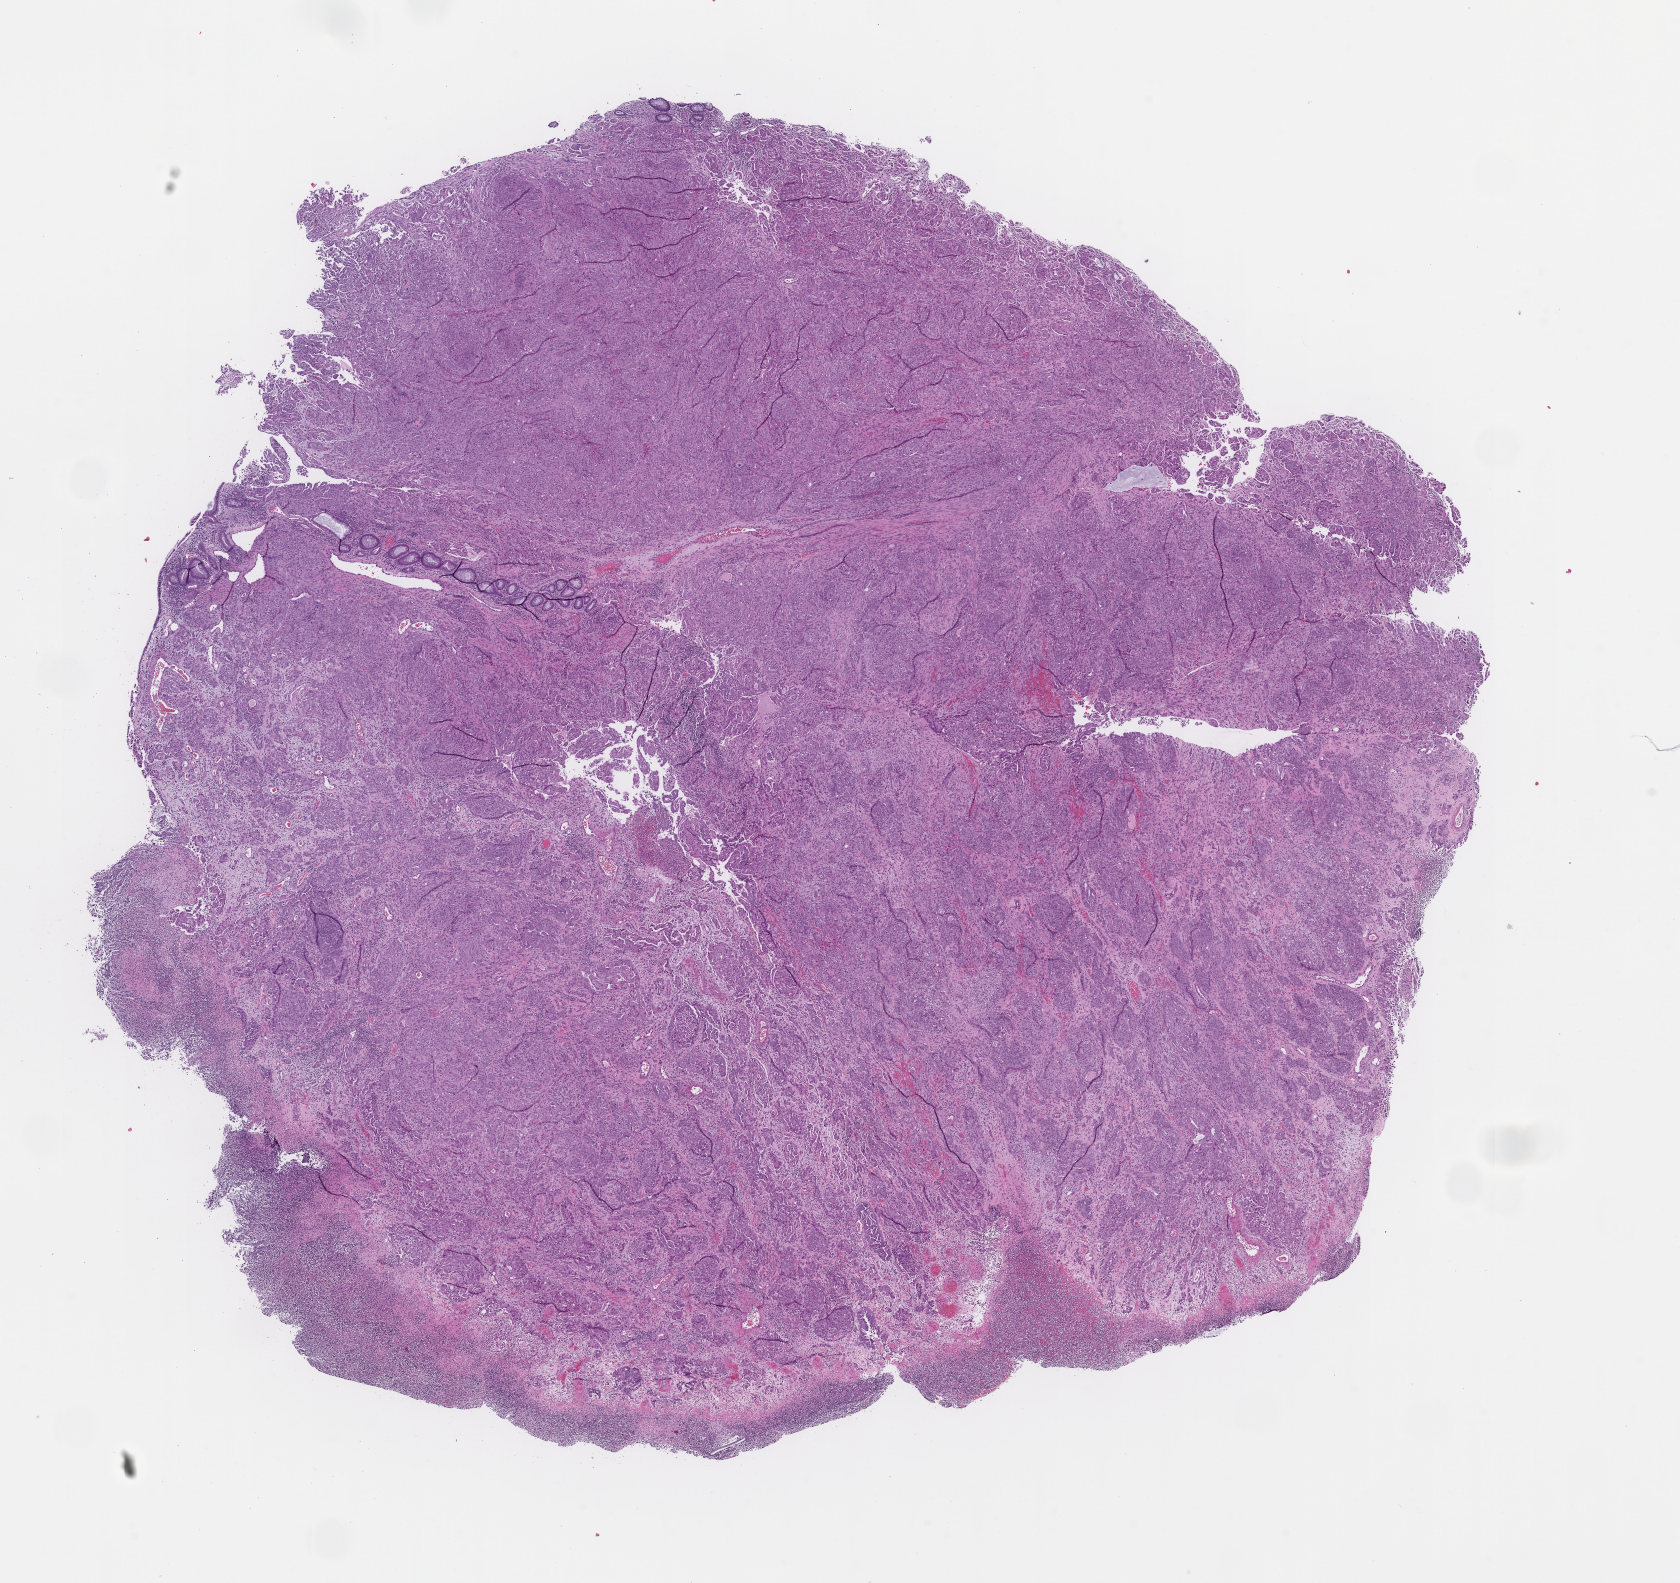
H&E whole-slide image — whole scanned area (about 13.6 x 12.8 mm) shown as a low-resolution overview; FFPE section; collected at disease progression. Patient: female.
This section: metastasis (sampled organ not recorded). Patient diagnosis (primary): Ovarian Carcinoma.